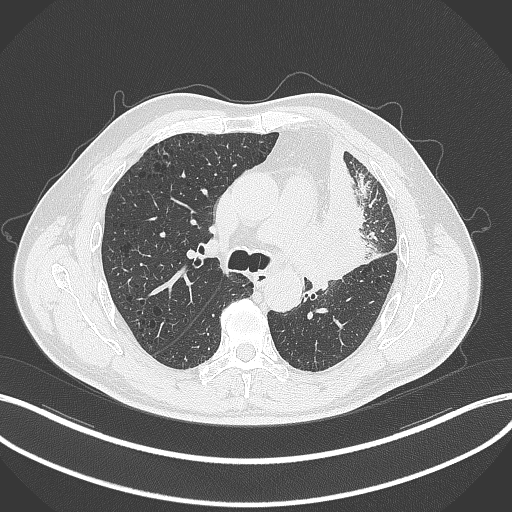
Chest CT, one axial slice; position 193 of 297 along the scan axis; reconstruction kernel B70f; lung window (W 1500 / L -600 HU); 1 mm slice thickness; 512 × 512 image matrix, field of view 400 × 400 mm. Patient: male, 68 years. Case-level facts recorded for this patient, not image findings: clinical TNM (as recorded): T3 N3 M1.
Outlined on this slice (bounding box drawn by a radiologist):
- lung tumour (recorded histology: adenocarcinoma): box from (x=308, y=147) to (x=386, y=284) px